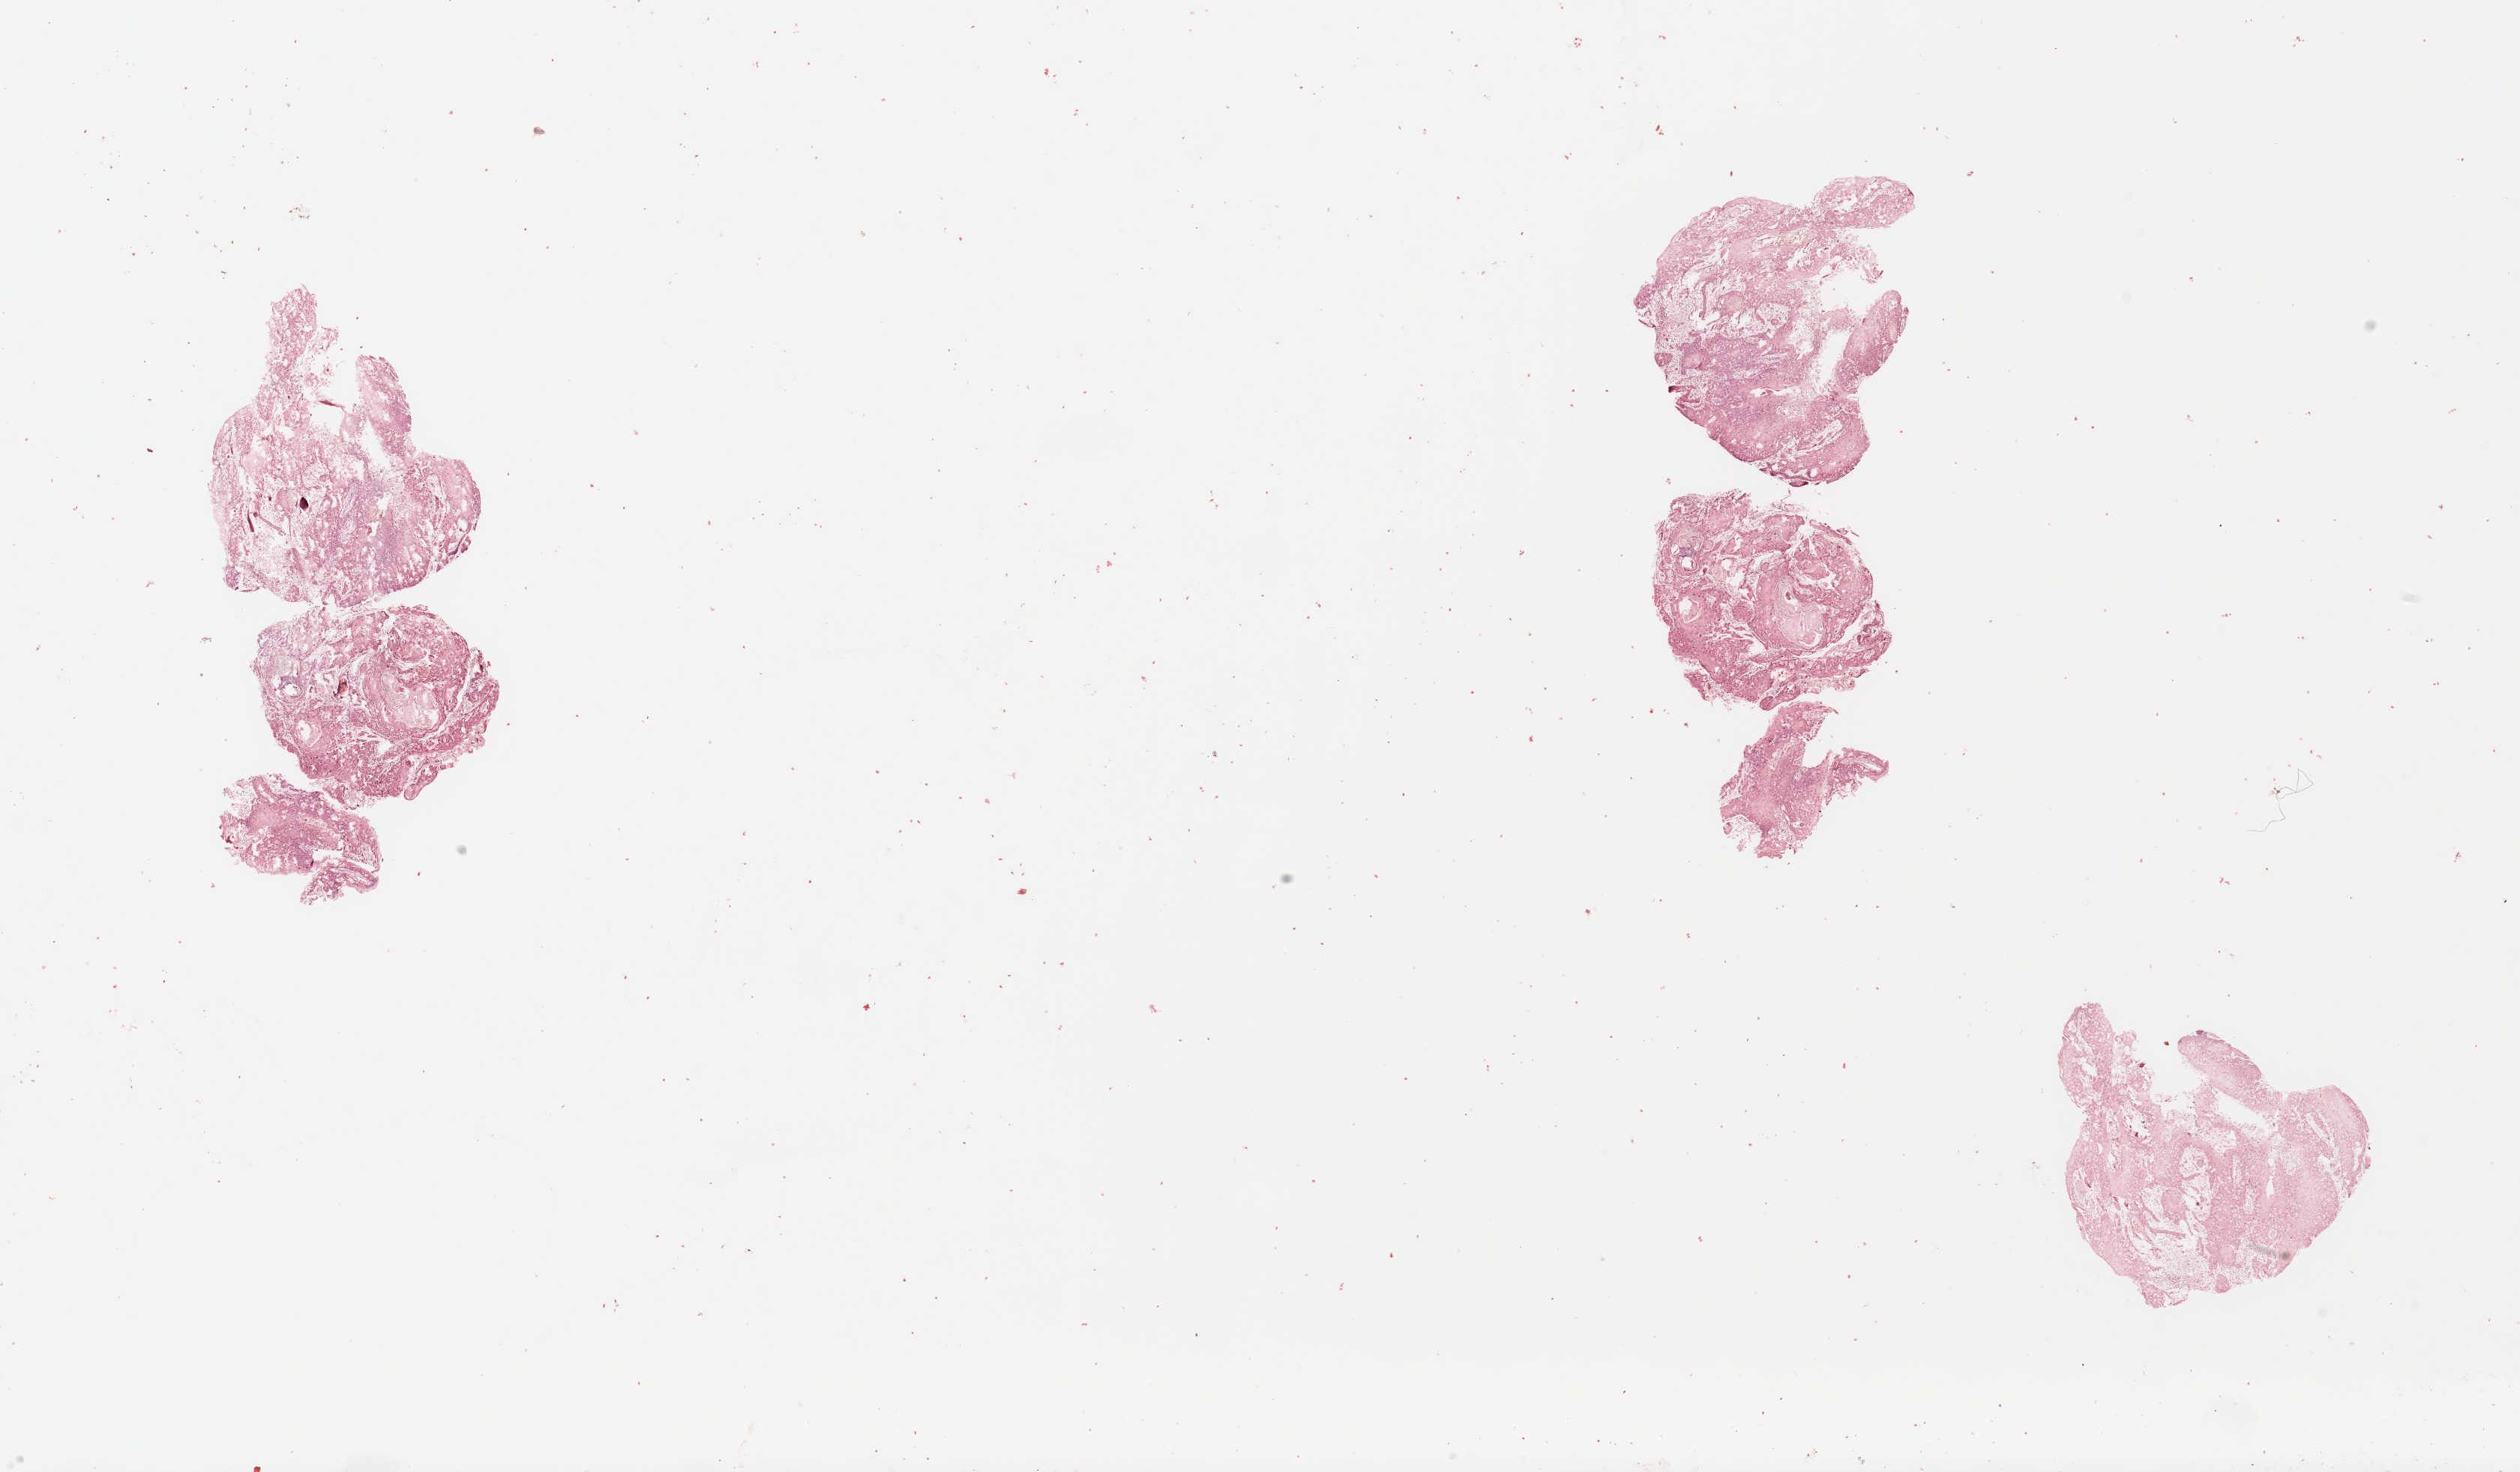
H&E whole-slide image — a low-resolution overview of the entire scanned area, about 26.6 x 15.5 mm (from a 20x scan); tumour tissue sample, sampled site: tongue. Patient: male, age 64 years. Histologic grade: G2 (moderately differentiated). Slide review estimates, as recorded: tumour nuclei 80%, necrosis 2%.
- histologic diagnosis: Squamous cell carcinoma, NOS
- AJCC pathologic stage: III
- primary tumour site (as recorded): oral cavity